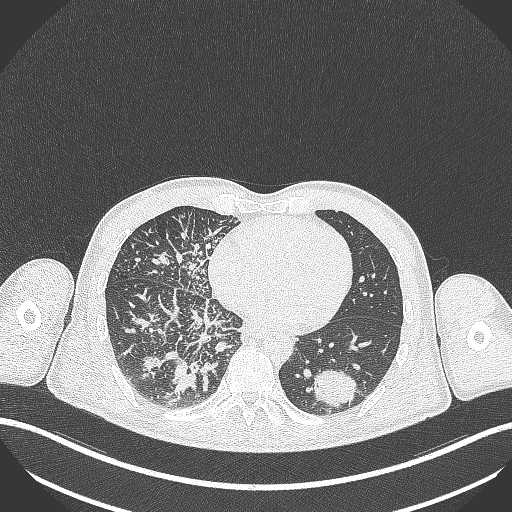
Chest CT, one axial slice; position 111 of 348 along the scan axis; 120 kVp; lung window (W 1500 / L -600 HU); 1 mm slice thickness; 512 × 512 image matrix, field of view 400 × 400 mm. Patient: male, 49 years. Case-level facts recorded for this patient, not image findings: clinical TNM (as recorded): T2b N1 M0.
Annotated regions visible in this slice (rectangle marked by the reading radiologist):
- lung tumour (recorded histology: adenocarcinoma): bounding box [x1, y1, x2, y2] px = [305, 367, 364, 410]